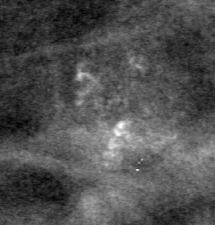
Crop from a digitized film mammogram around one marked abnormality, left breast, CC view, BI-RADS breast density category 3 (scale 1–4).
Finding: calcifications, morphology pleomorphic, distribution clustered; BI-RADS assessment category 4; subtlety rating 1 on a 1 (subtle) to 5 (obvious) scale; pathology (as recorded): benign.